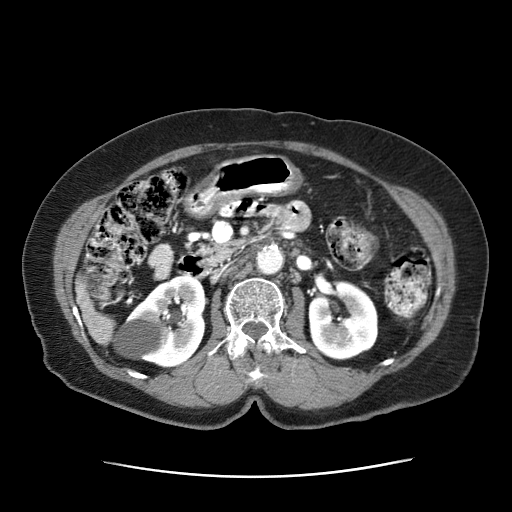
Contrast-enhanced abdominal CT (liver protocol), one axial slice. Position 10 of 63 along the scan axis. Reconstruction kernel STANDARD. 120 kVp. Intravenous contrast given. Soft-tissue window (W 400 / L 40 HU). 512 × 512 image matrix. Patient: female, 79 years. From the clinical record (not read from this slice): diagnosis: hepatocellular carcinoma (patient treated with transarterial chemoembolisation; whether this scan precedes or follows treatment is not stated here); TNM stage (as recorded): Stage-II; Child-Pugh class: B; tumour differentiation: well differentiated; tumour nodularity: multinodular.
Structures marked on this image (semi-automatically segmented with operator editing):
- abdominal aorta: bounding box [x1, y1, x2, y2] px = [256, 245, 283, 274]
- liver parenchyma outside the tumour (the mass and vessels are separate outlines, so this box may not span the whole liver): [77, 292, 115, 345]